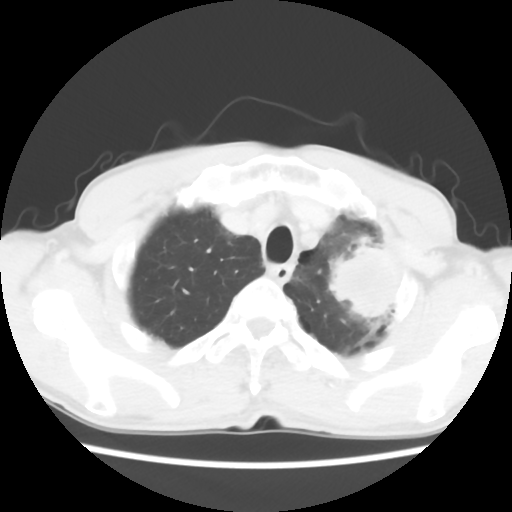
Chest CT, one axial slice. Position 51 of 60 along the scan axis. Reconstruction kernel STANDARD. 120 kVp. Lung window (W 1500 / L -600 HU). 5 mm slice thickness. 512 × 512 image matrix. Male patient, age 64 years. From the clinical record (not read from this slice): clinical TNM (as recorded): T3 N3 M0.
Outlined on this slice (rectangle marked by the reading radiologist):
- lung tumour (recorded histology: adenocarcinoma): bounding box [x1, y1, x2, y2] px = [322, 233, 403, 333]